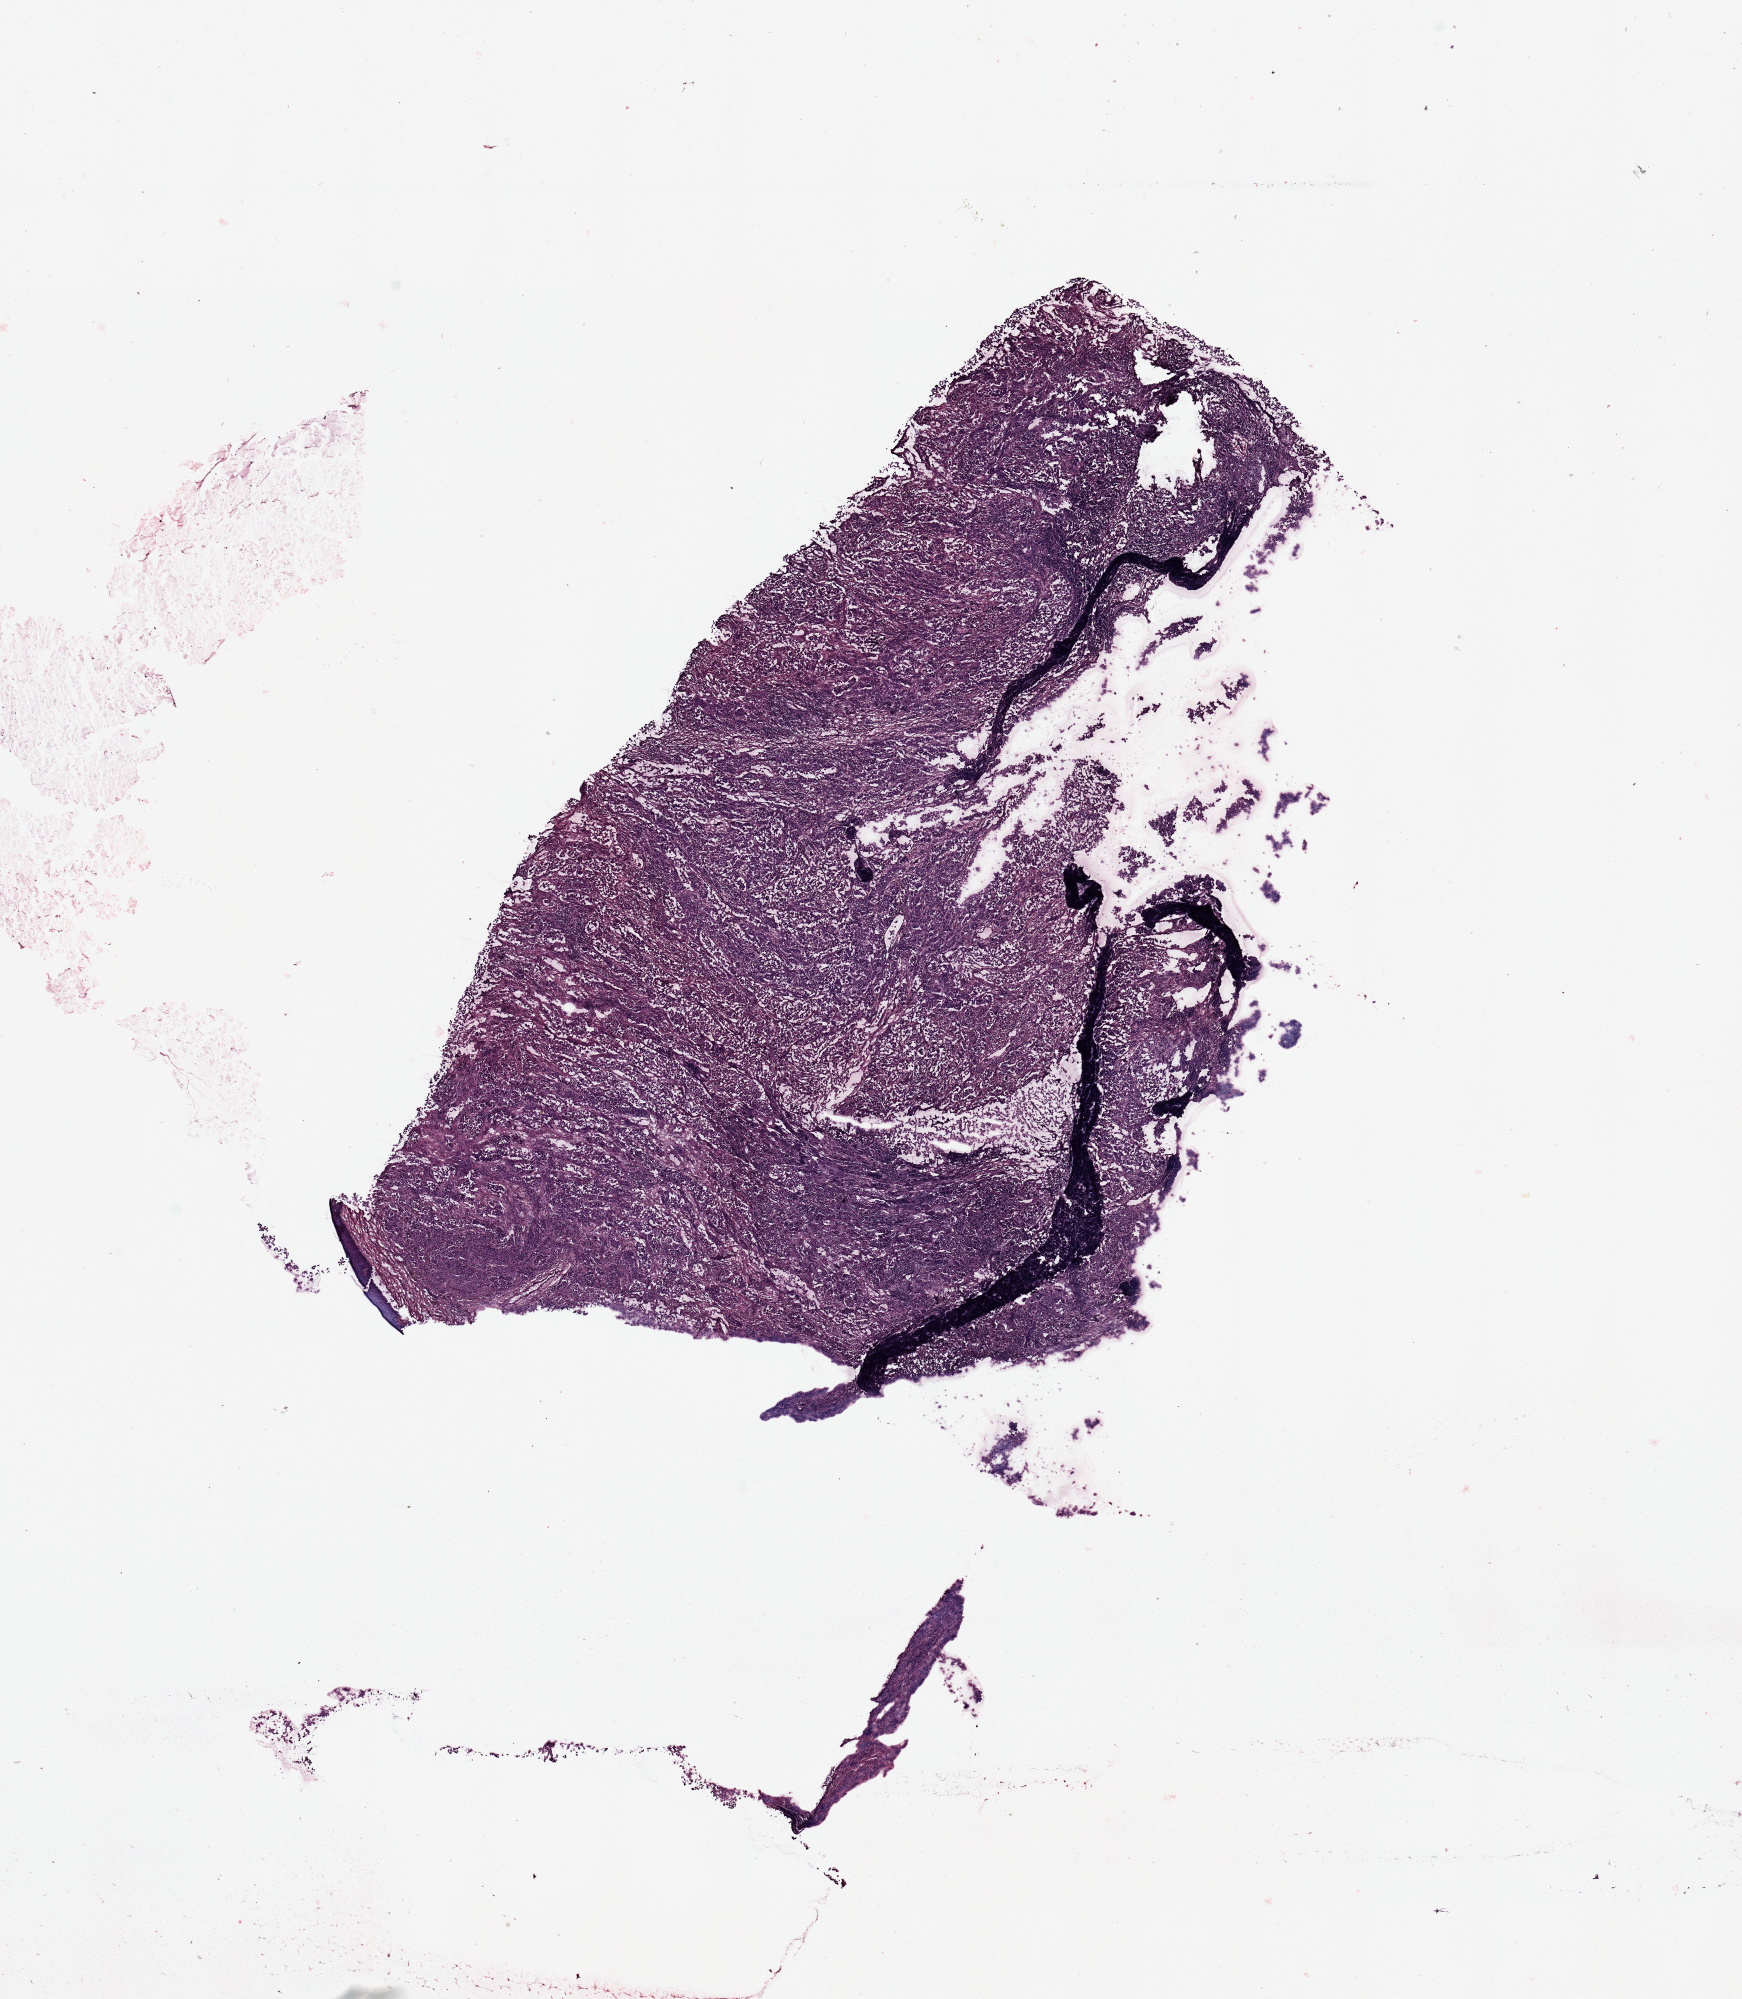
H&E-stained whole-slide image, shown as a low-resolution overview of the whole scanned area (about 13.8 x 15.8 mm, acquisition: 20x scan), melanoma tumour tissue; sampled site not recorded. 51-year-old female patient.
Primary tumour site (as recorded): extremities. Patient diagnosis (cohort enrolment): cutaneous melanoma (skin).